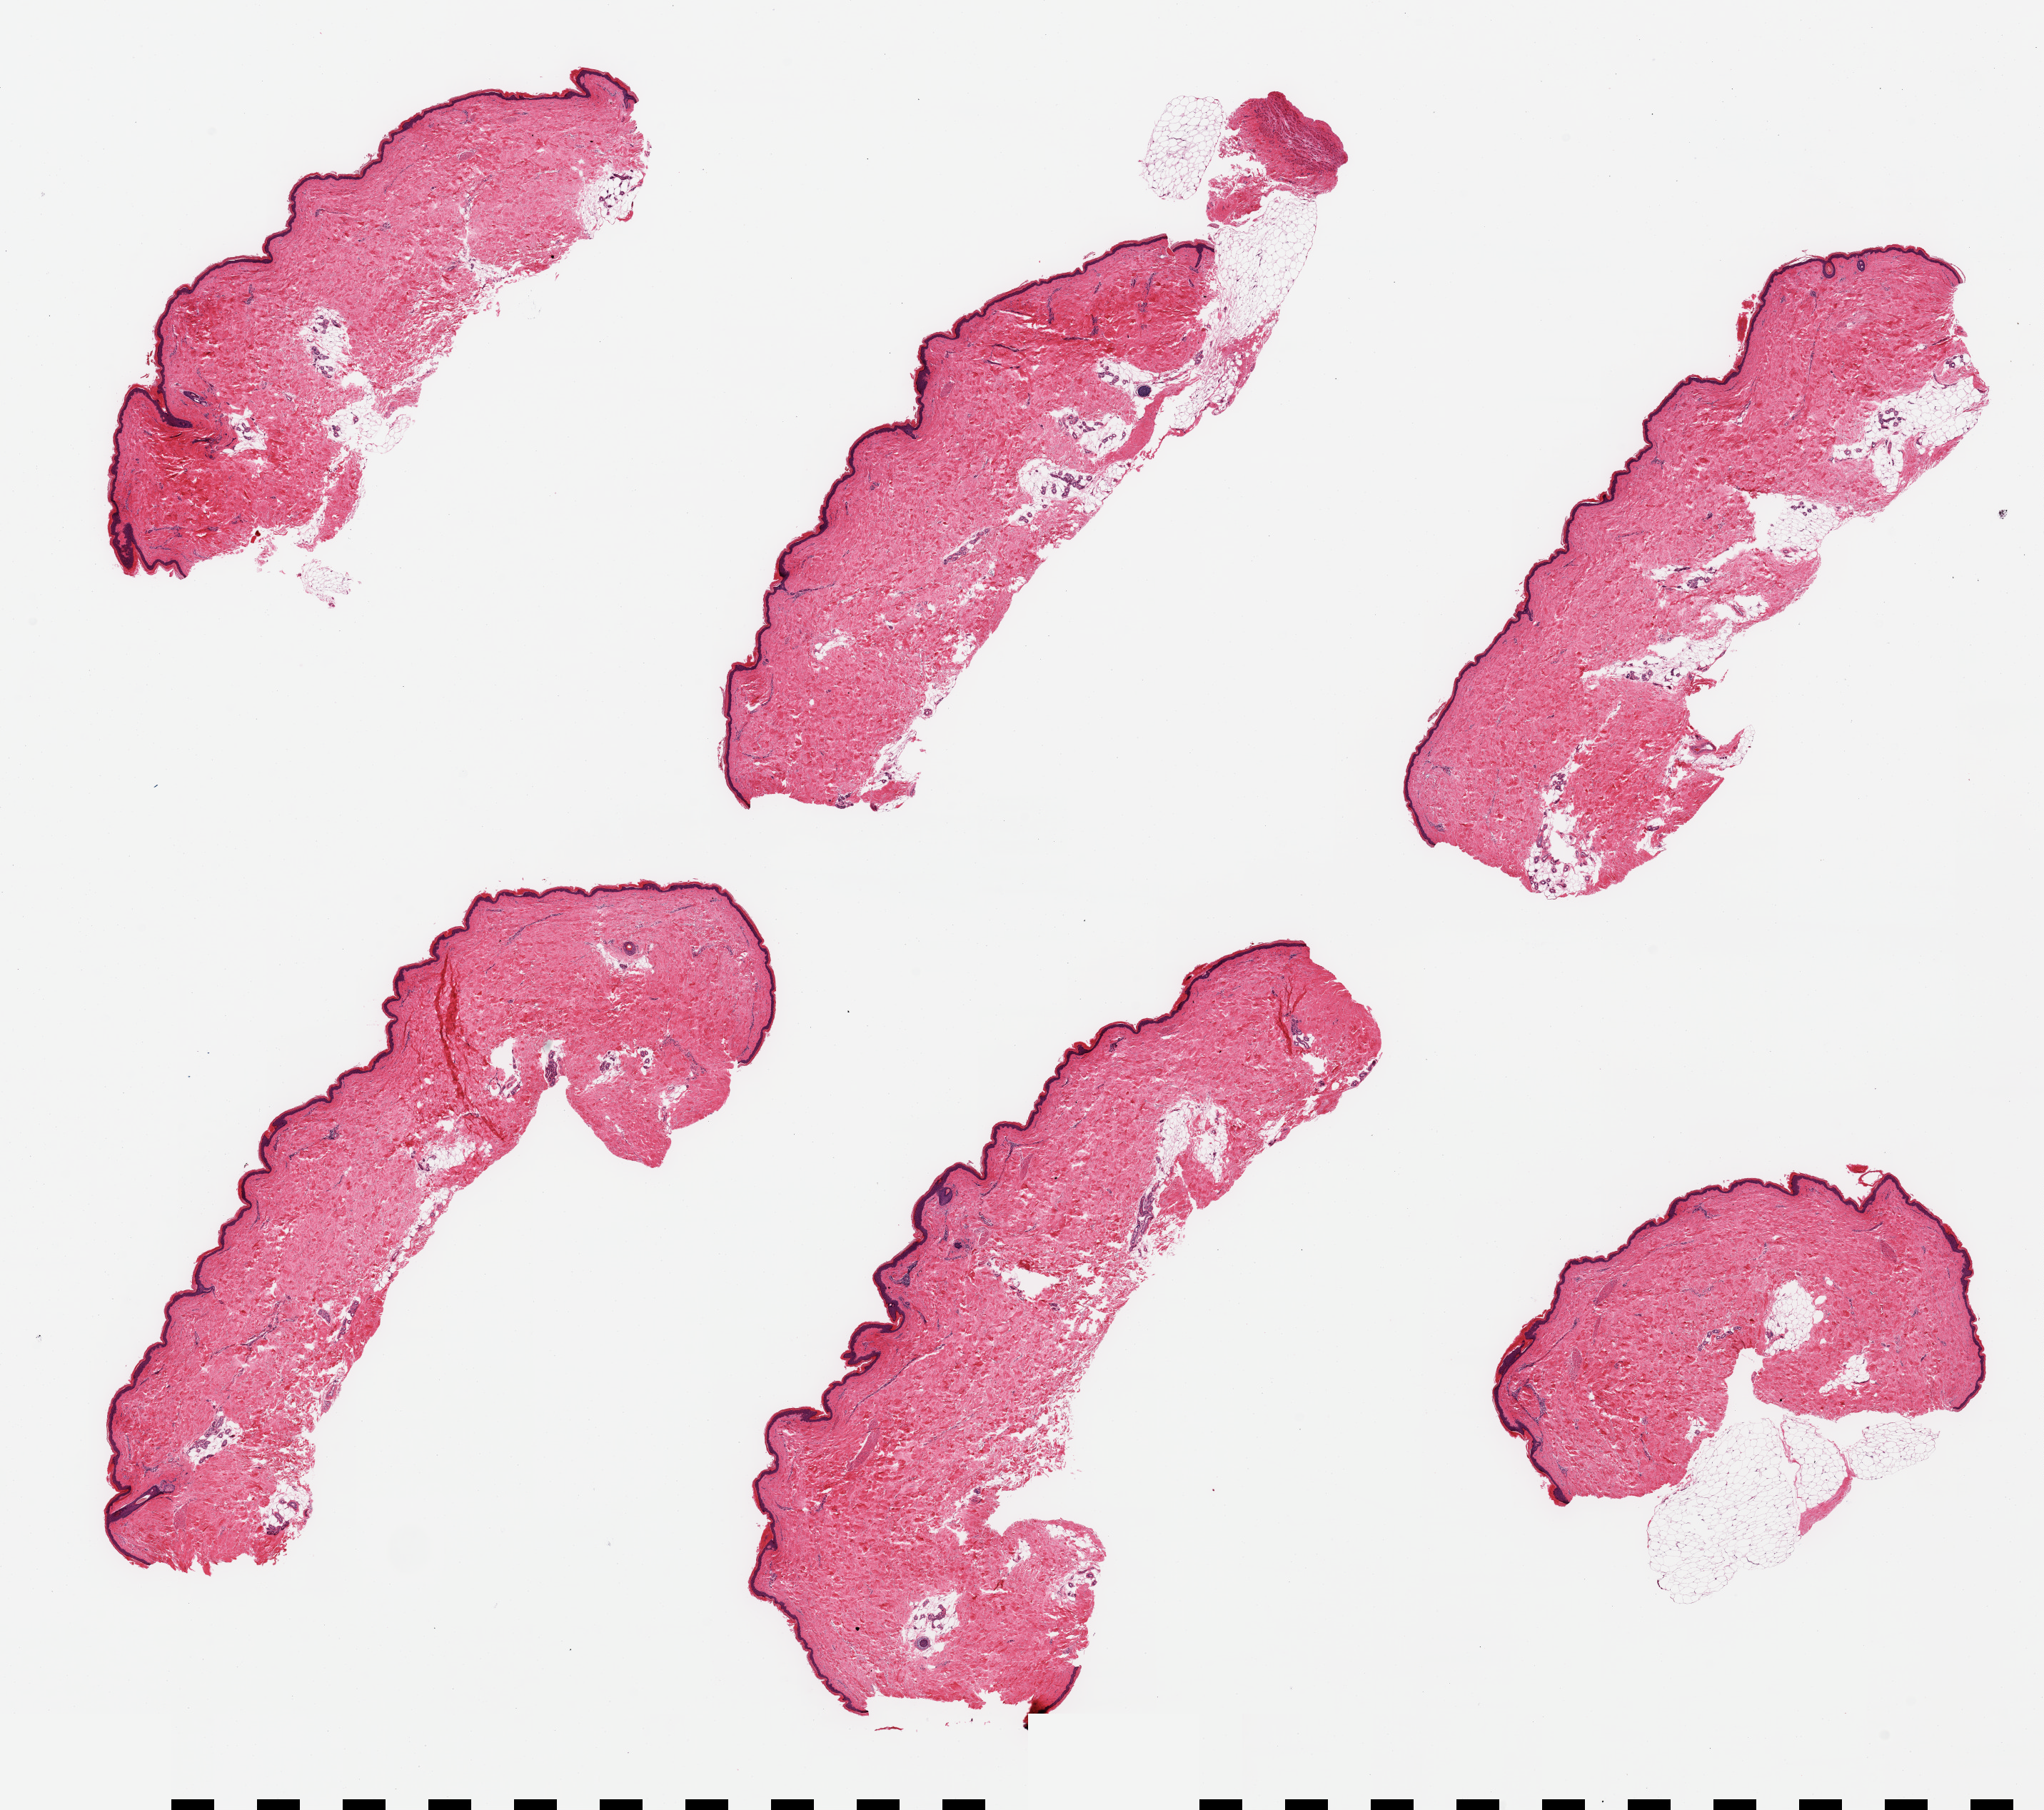
Digitized haematoxylin and eosin-stained section, brightfield — a low-resolution overview of the entire scanned area, about 22.6 x 20.0 mm; PAXgene-fixed, paraffin-embedded tissue; sampled site (target tissue): skin of lower leg; tissue donor sample. Female donor.
Pathologist's review note for this sample: 6 pieces, squamous epithelium is ~30-35 microns; moderate dermal fat.